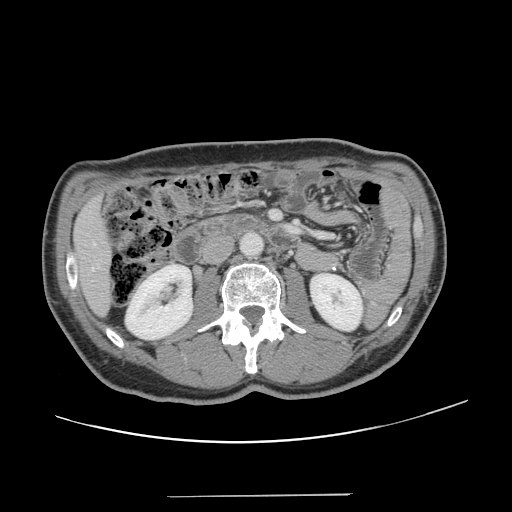
Contrast-enhanced abdominal CT, one axial slice. Position 51 of 131 along the scan axis. Soft-tissue window (W 400 / L 40 HU). 2.5 mm slice thickness. 512 × 512 image matrix, field of view 403 × 403 mm. Male patient, age 60 years. Case-level facts recorded for this patient, not image findings: diagnosis: colorectal cancer liver metastases, imaged before liver resection; multiple liver metastases: no; largest metastasis: 2.5 cm; disease in both lobes: no.
Structures marked on this image (manually delineated by an expert):
- hepatic veins: bounding box (x1, y1, x2, y2) in pixels: (92, 244, 95, 269)
- liver: (76, 200, 110, 313)
- planned liver remnant (the part of the liver to remain after resection): (76, 200, 110, 313)